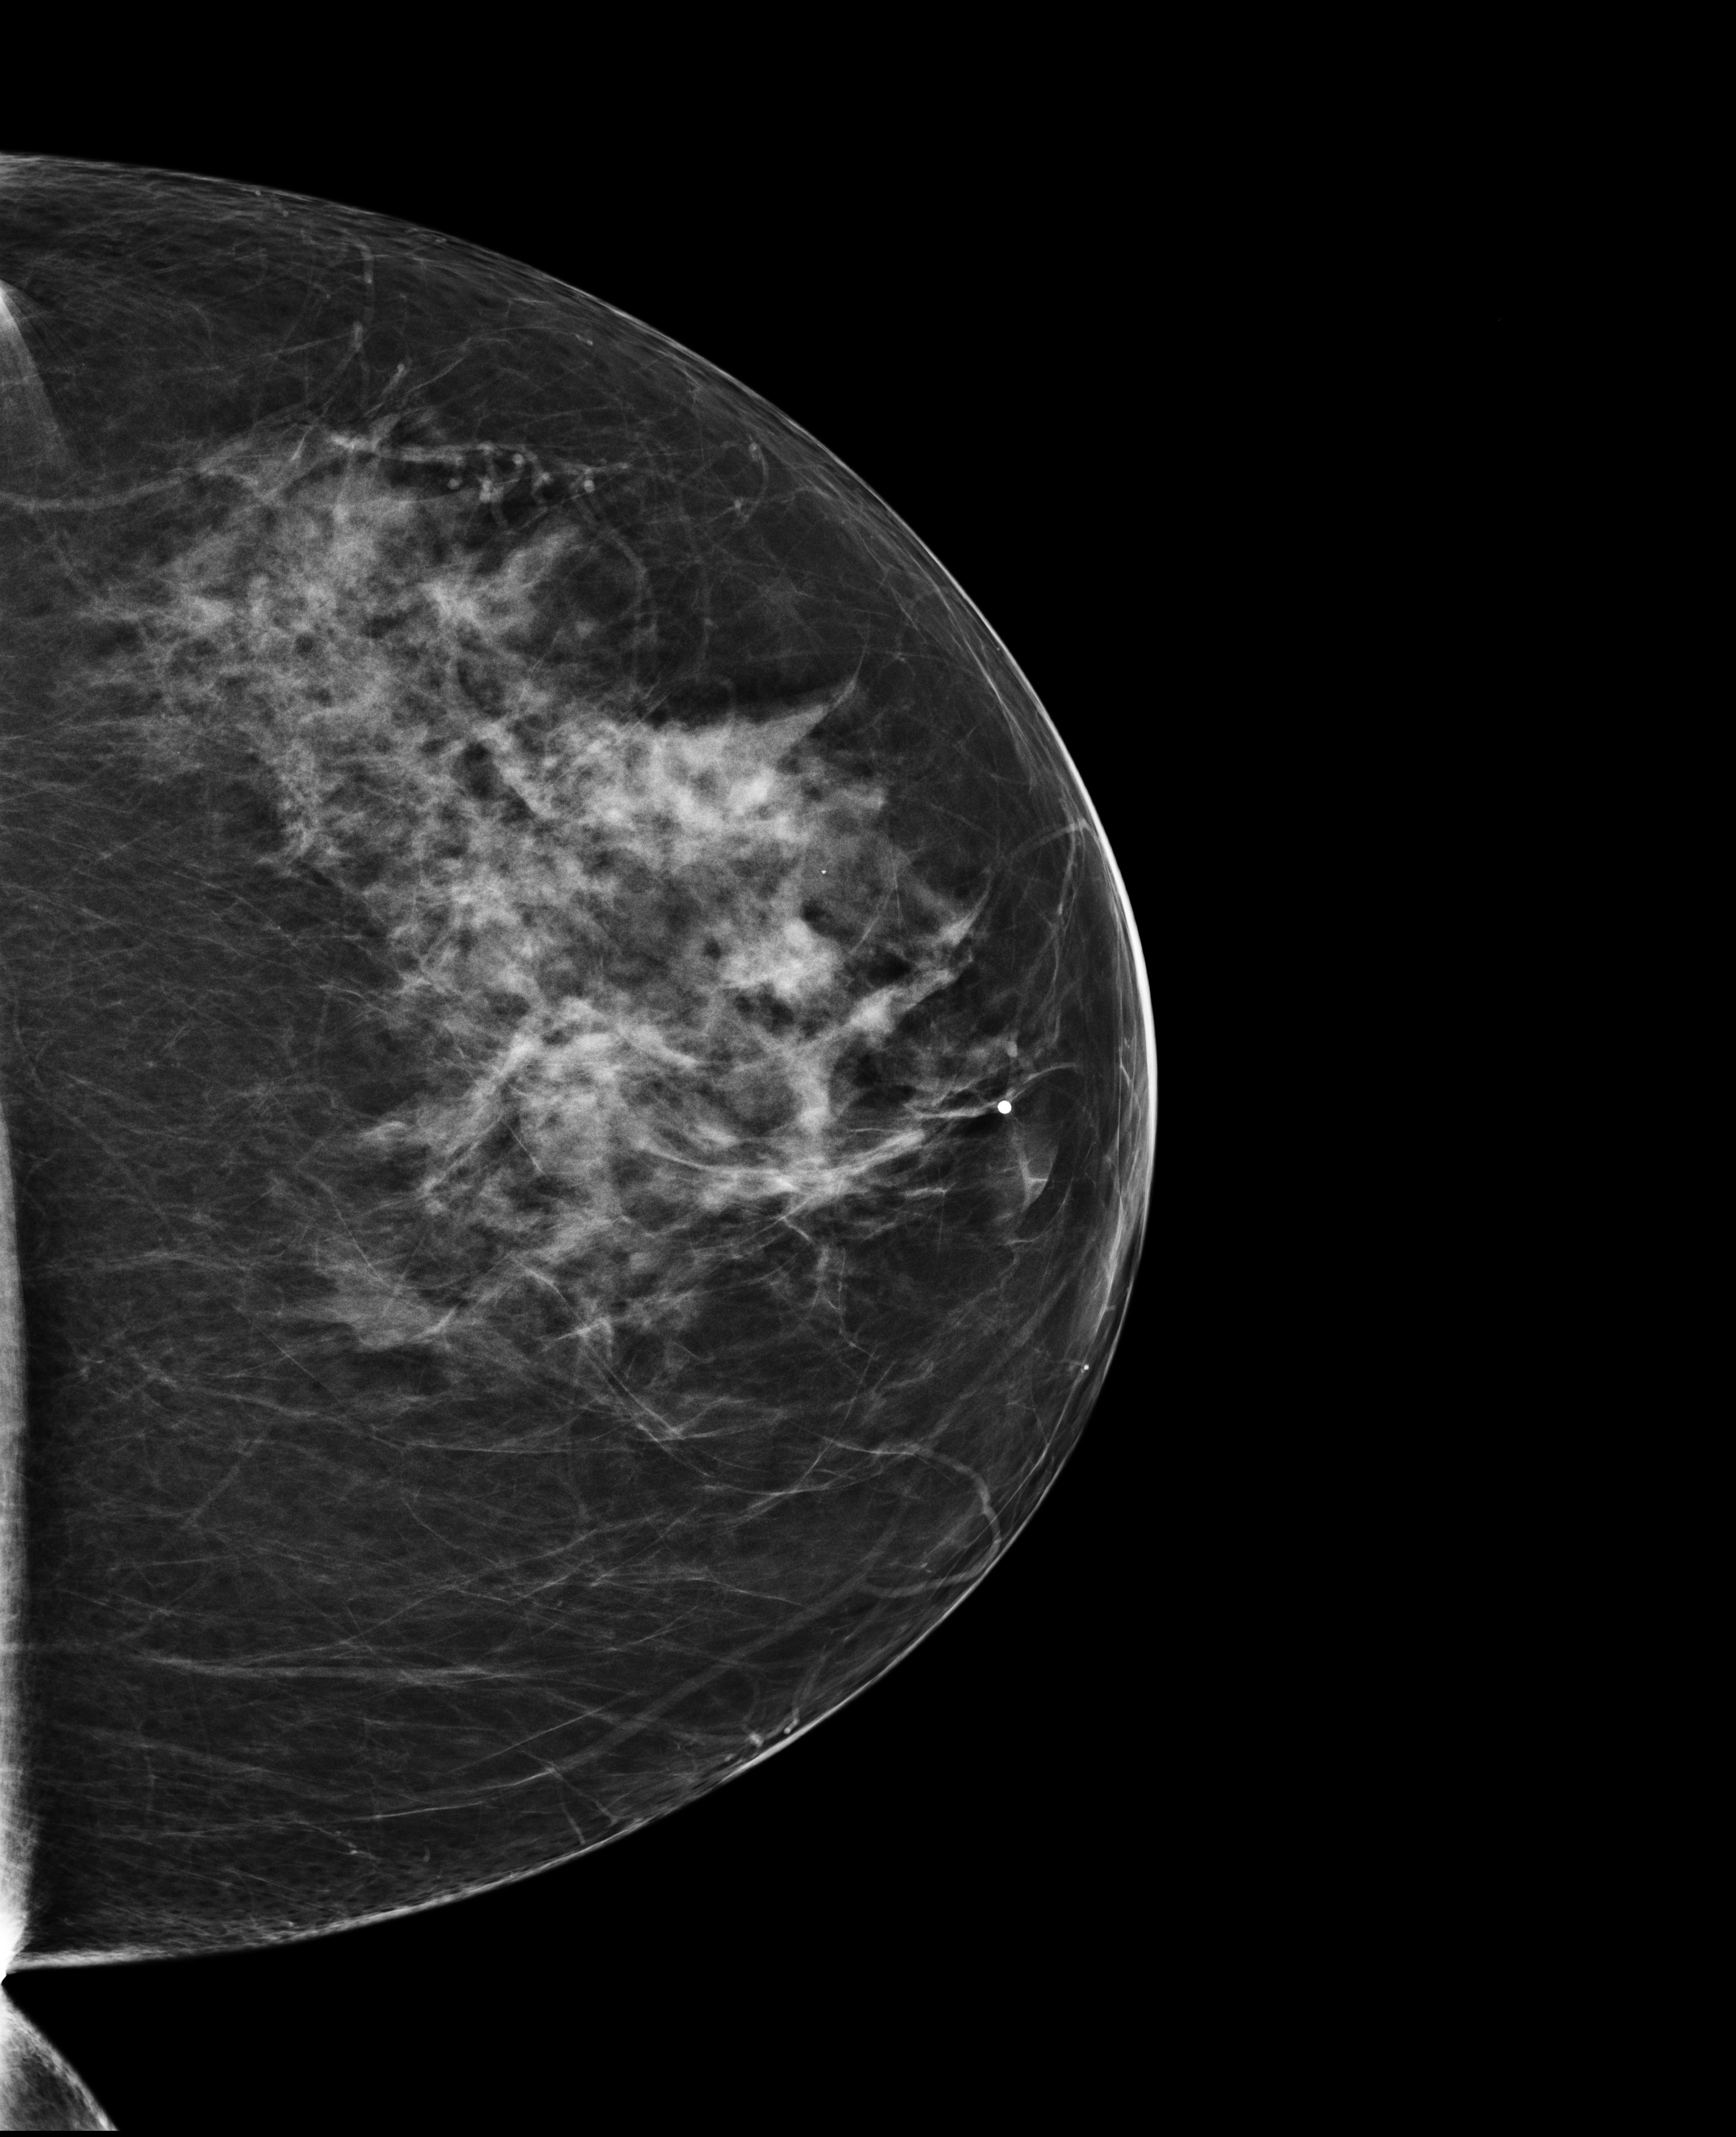
Annual screening mammography examination; compressed breast thickness 79 mm. Female patient, age 60 years.
Image type: full-field digital mammogram. Breast: left. Projection: craniocaudal (CC) view. BI-RADS breast density category at the screening exam (both breasts, scale 1–4): 3. Final BI-RADS category for the screening round (tomosynthesis exam, both breasts): category 1. Recall: no recall after this screen.